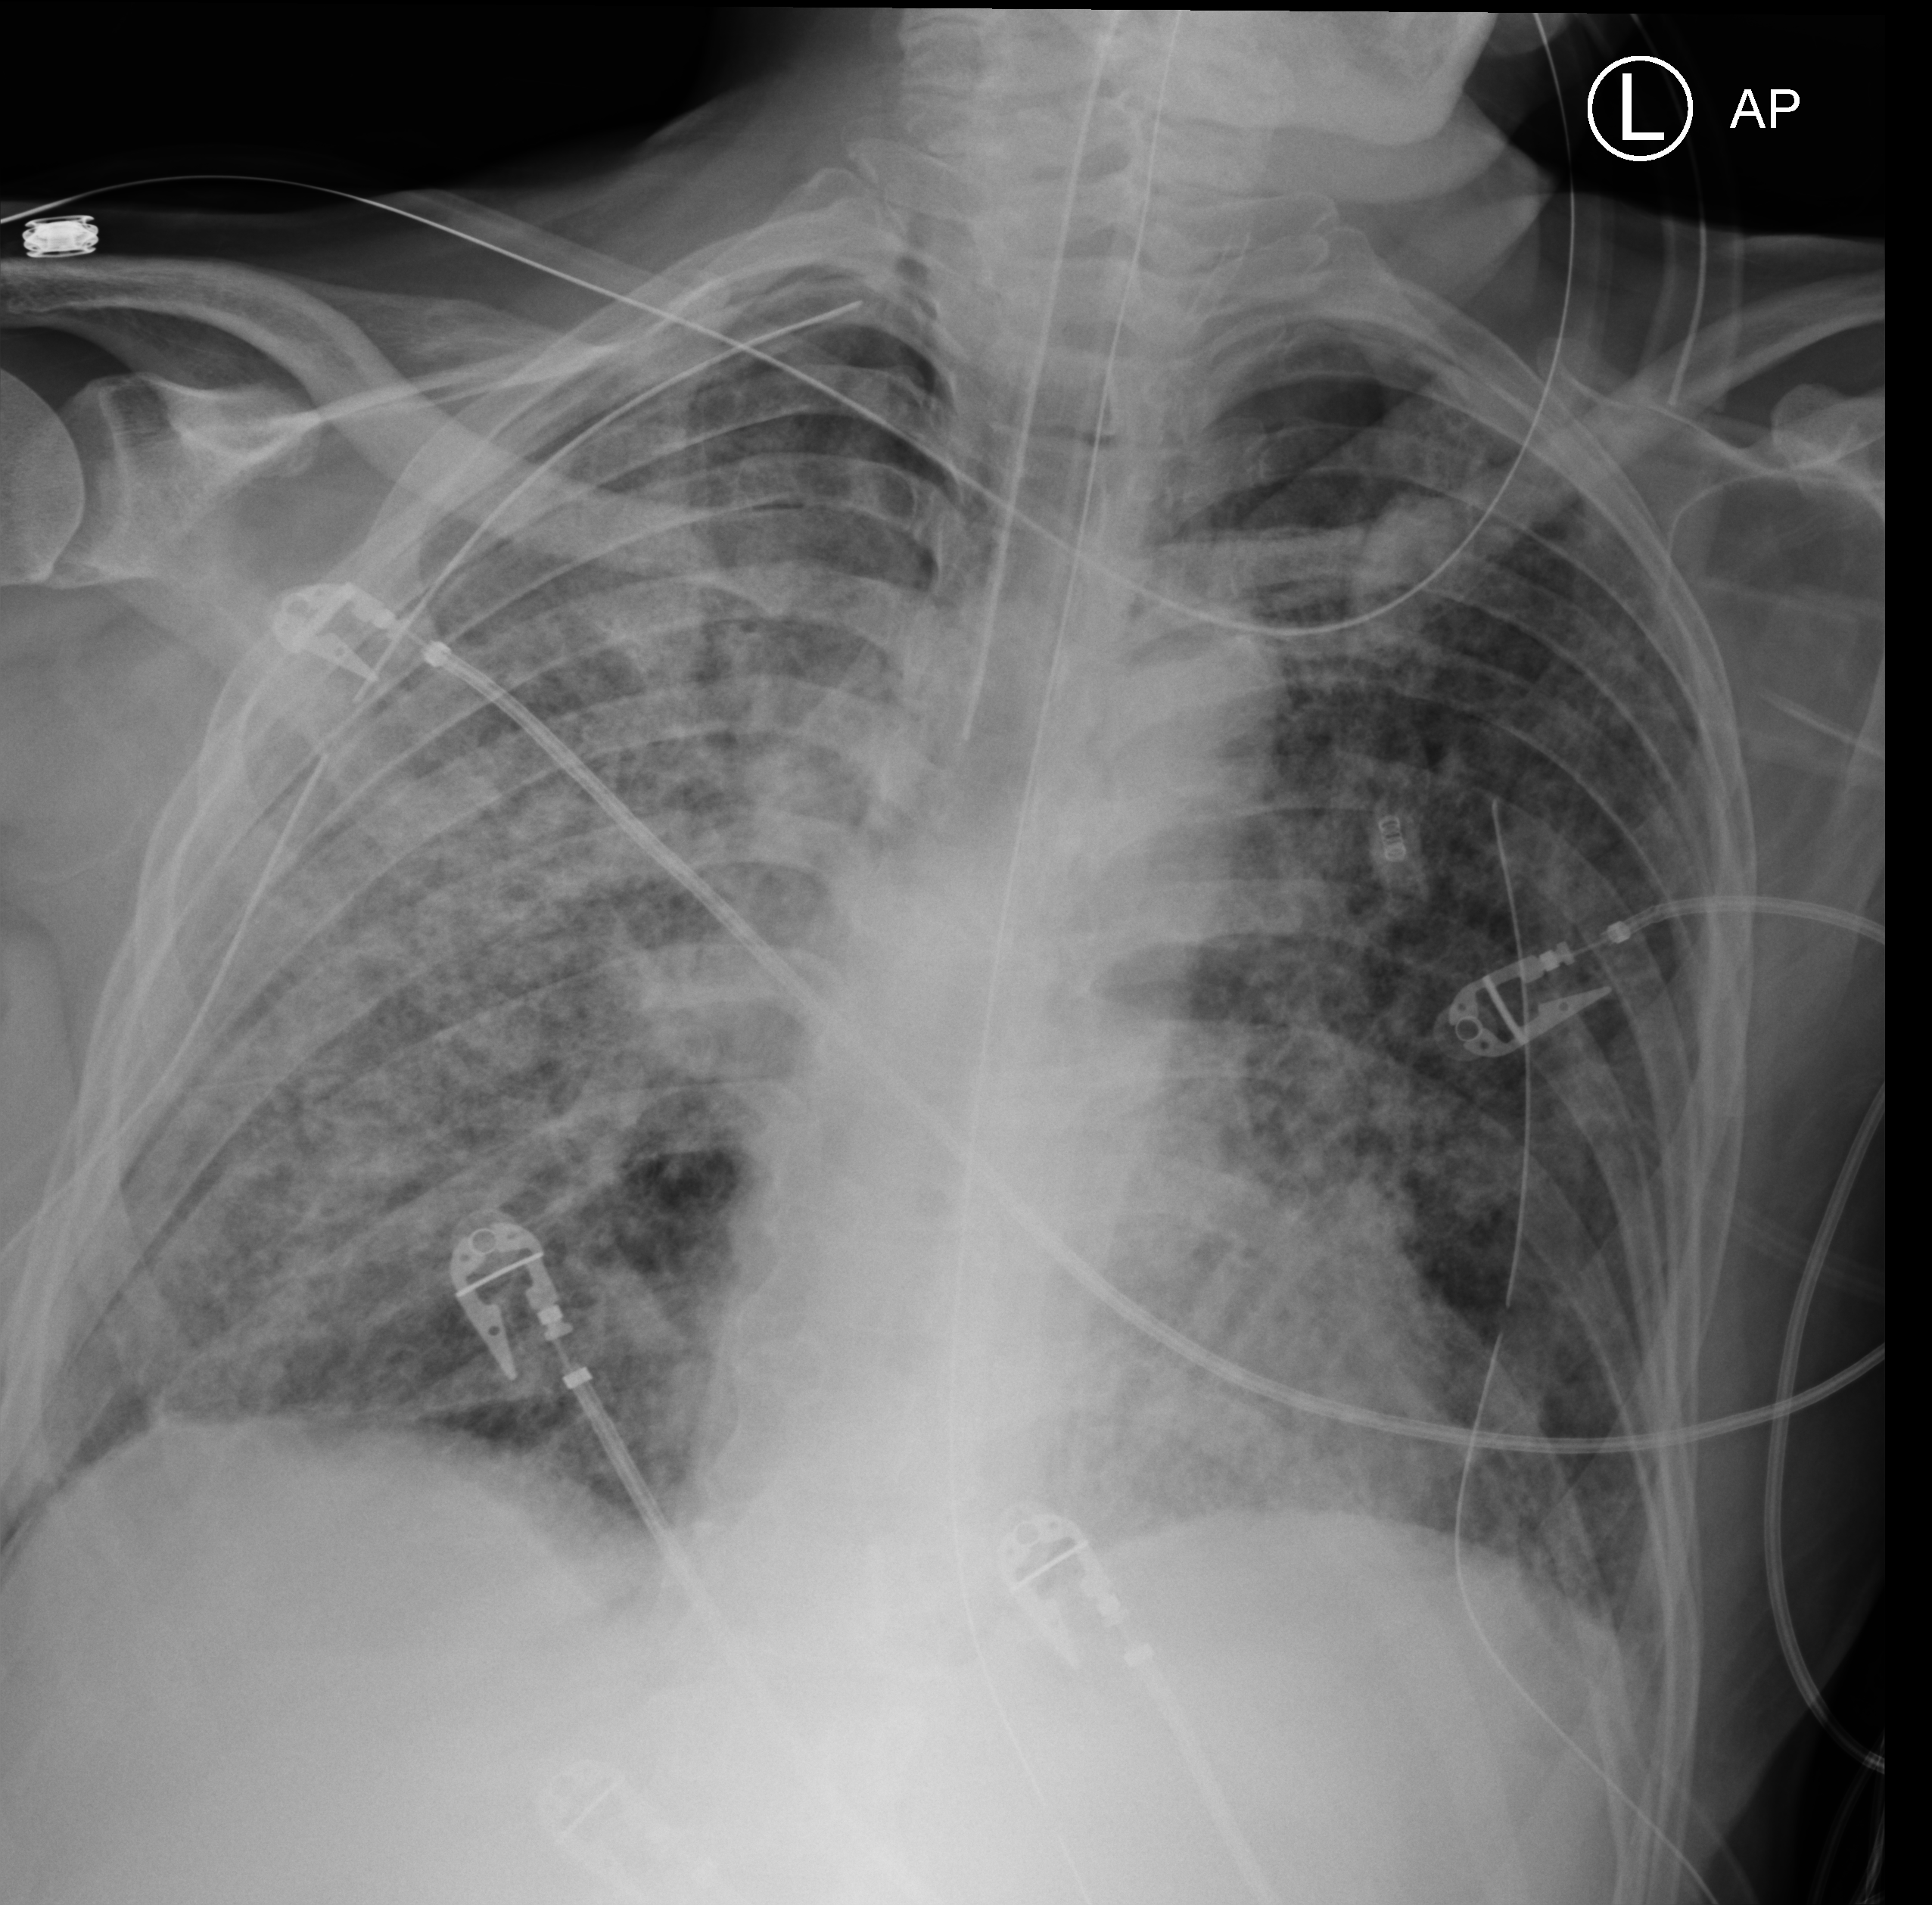
Bedside chest radiograph (computed radiography); anteroposterior (AP) projection. Patient hospitalised with COVID-19; male, aged 60–74 years.
From the hospital-stay record, not from the radiograph (when in the stay this image was taken is not recorded): admitted to intensive care during this hospital stay: yes; mechanically ventilated during this hospital stay: yes.